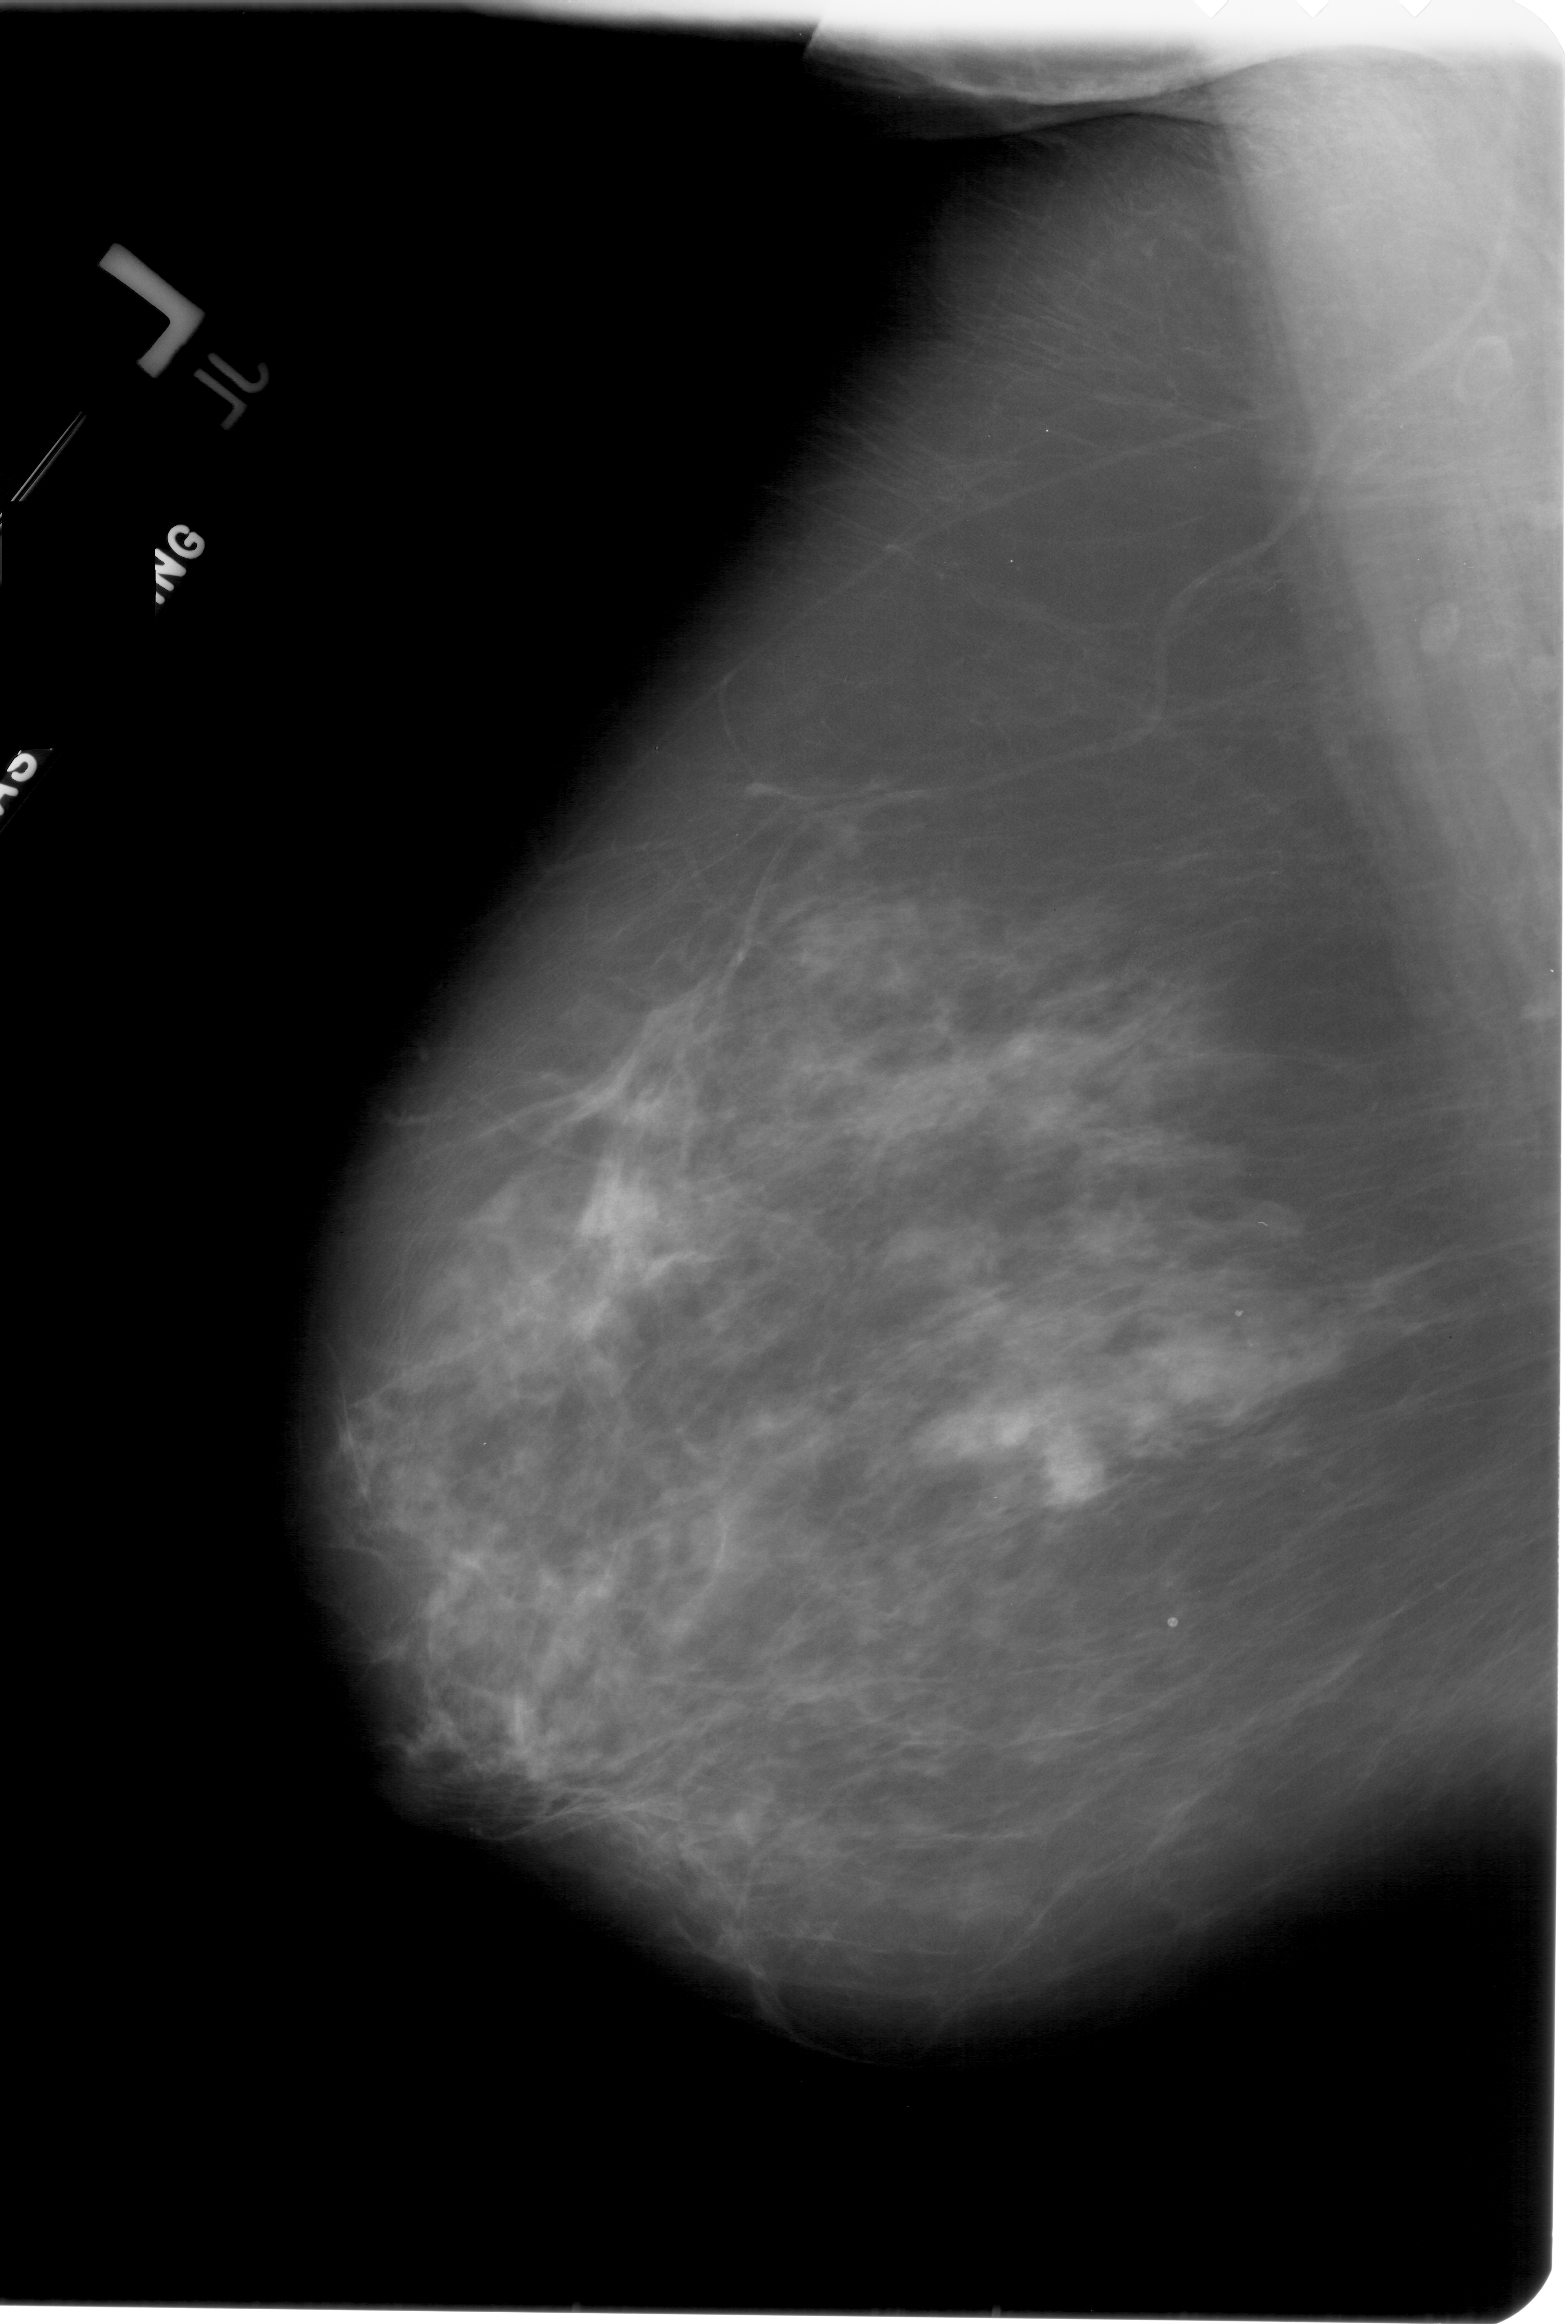
Scanned film-screen mammogram; left breast; MLO view; BI-RADS breast density category 3 (scale 1–4).
Abnormality record for this image: mass, shape irregular, margins spiculated; BI-RADS assessment category 5; subtlety rating 5 on a 1 (subtle) to 5 (obvious) scale; pathology result (as recorded, not read from the image): malignant.